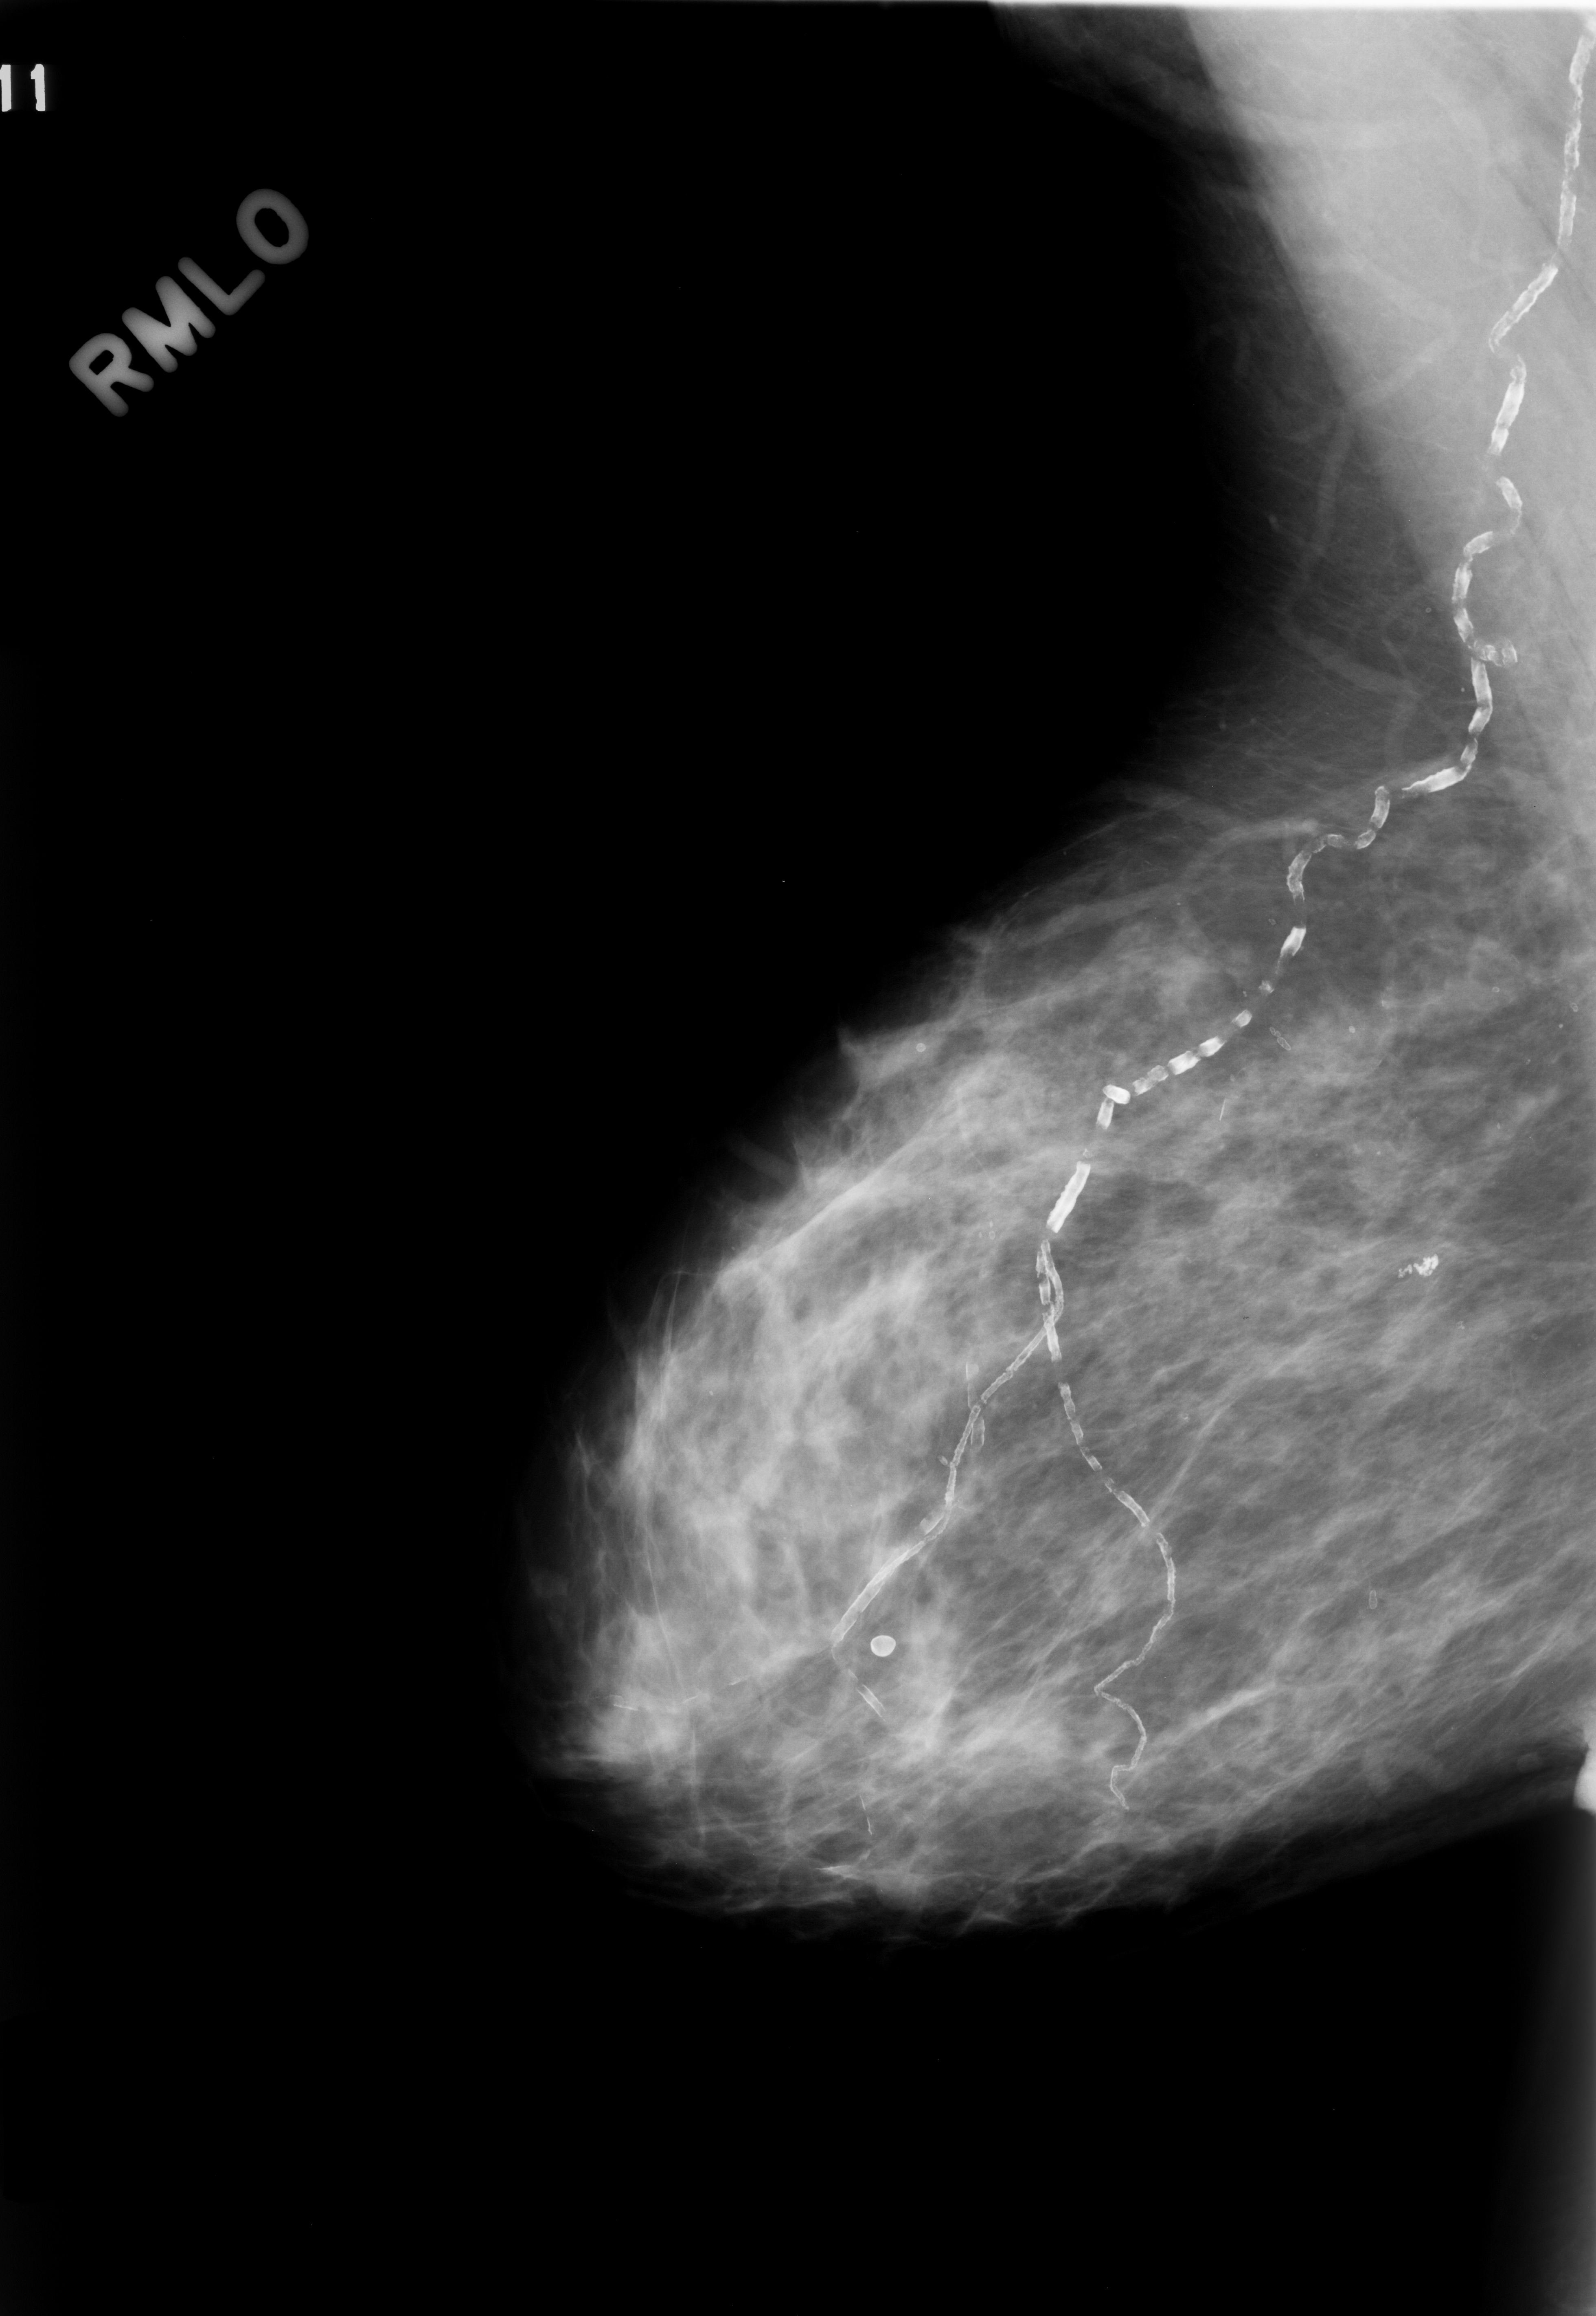
Digitized screen-film mammogram, right breast, MLO view, breast composition: scattered fibroglandular densities (BI-RADS density category 2 of 4).
Finding: calcifications, morphology pleomorphic, distribution clustered; BI-RADS assessment category 4; pathology result (as recorded, not read from the image): benign.